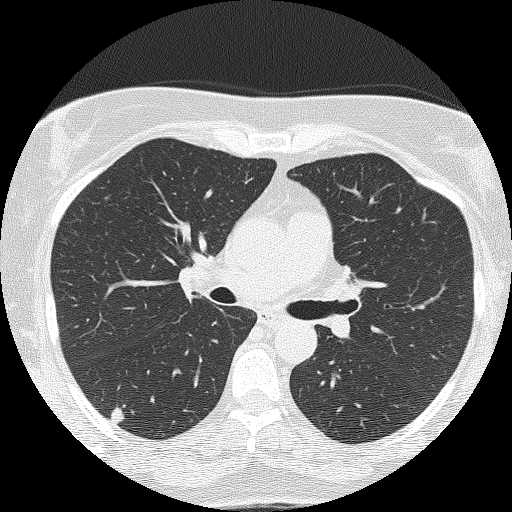
Low-dose screening chest CT, axial slice. Second screening round (one year after baseline). Lung window (W 1500 / L -600 HU). 2 mm slice thickness. 120 kVp. Slice 60 of 143 in the series. Female participant, aged 58 years at enrolment.
Expert reader's lesion annotation, bounding box (x1, y1, x2, y2) in pixels: (87, 395, 143, 434). The screening reader recorded 2 non-calcified nodules or masses ≥4 mm on this exam (right upper lobe, right upper lobe); which of them this box marks is not recorded. Official screen result: positive, other.